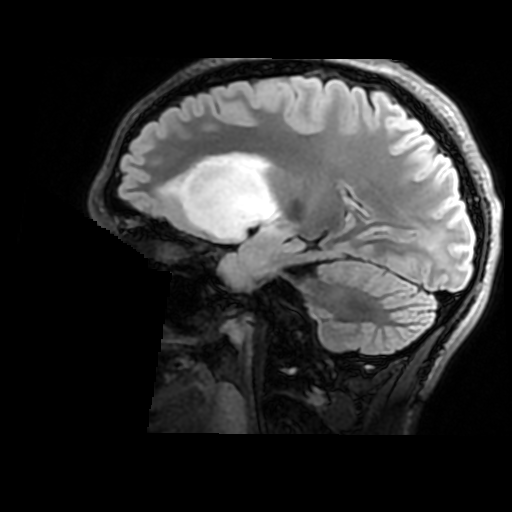
Brain MRI from a brain-tumour surgery series, one sagittal slice; position 107 of 176 along the scan axis; T2 FLAIR; 512 × 512 image matrix, field of view 240 × 240 mm. From the clinical record (not read from this slice): histopathology: Astrocytoma; WHO grade: 2; IDH mutation: yes; tumour location: Right Insular.
Structures marked on this image (outlined manually by an expert reader):
- tumour: bounding box <171,153,281,239> (left, top, right, bottom; pixels)